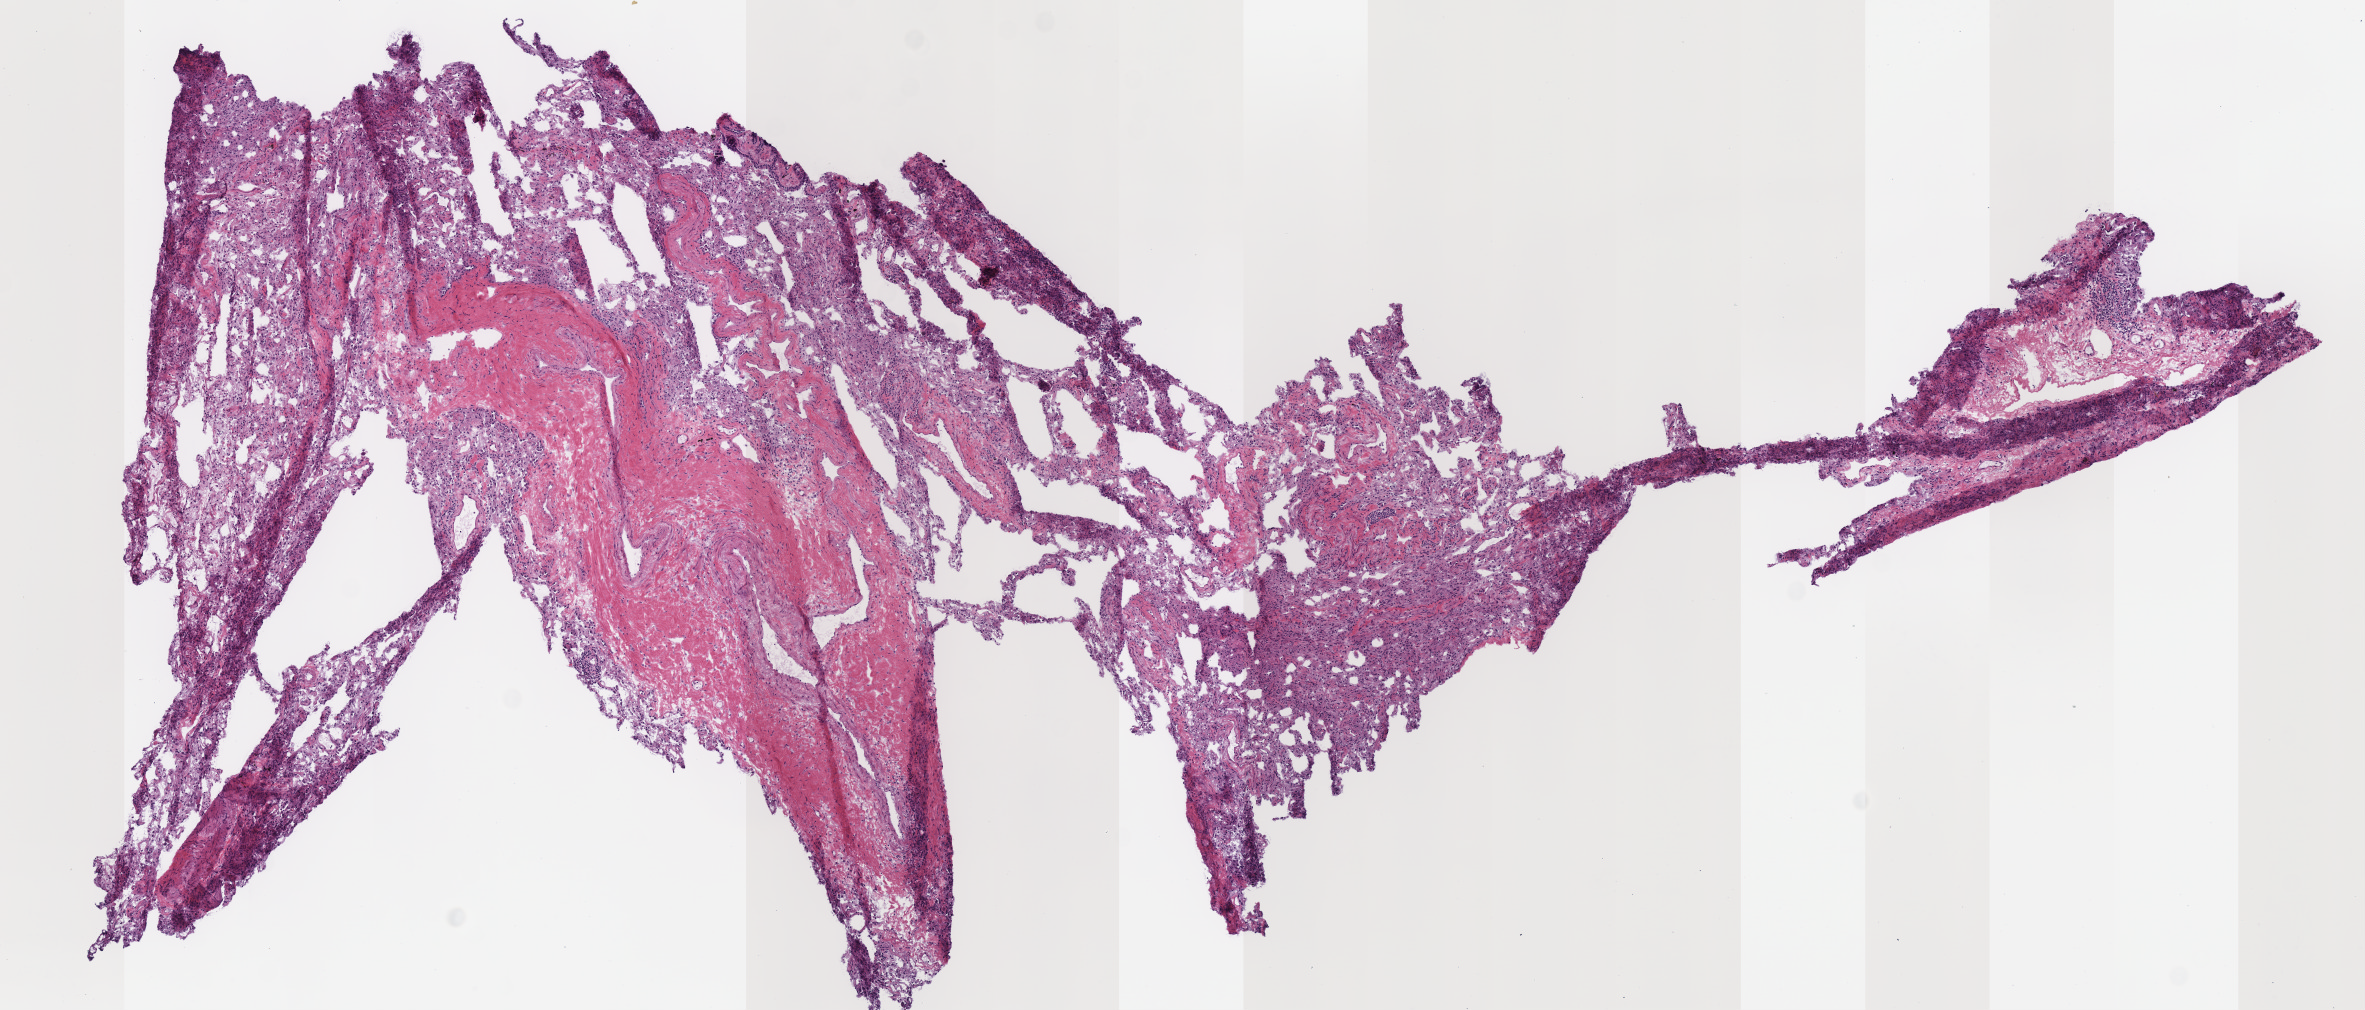
H&E-stained whole-slide image — a low-resolution overview of the entire scanned area, about 9.3 x 4.0 mm. Frozen section from the top of the tissue portion. Solid tissue normal (non-tumour tissue) sample from the lung. Female patient; age at initial diagnosis 73 years. Infiltration values recorded for this section: lymphocyte infiltration 3%, monocyte infiltration 2%, neutrophil infiltration 0%.
This section: solid tissue normal sample (biorepository sample class). Patient diagnosis: Adenocarcinoma with mixed subtypes (upper lobe, lung).